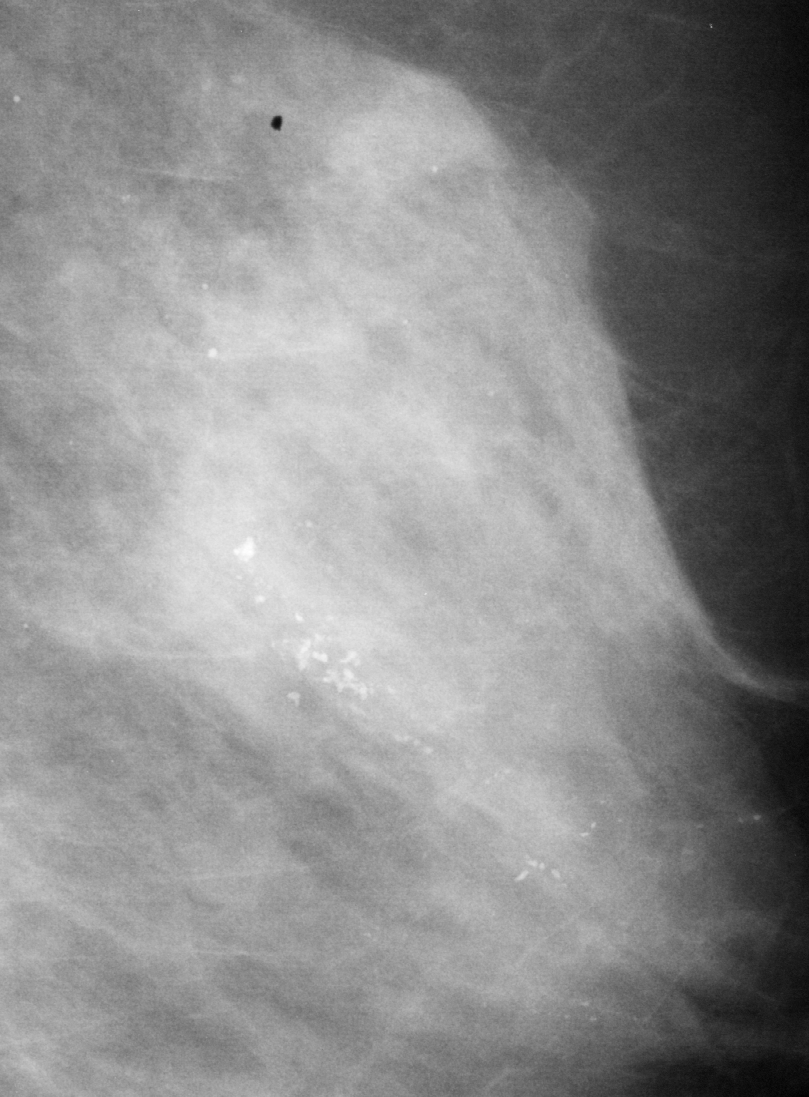
Cropped region of a digitized screen-film mammogram centred on a radiologist-marked abnormality, left breast, MLO view, BI-RADS breast density category 3 (scale 1–4).
Marked abnormality: calcifications, morphology pleomorphic, distribution segmental; BI-RADS assessment category 5; pathology (as recorded): malignant.